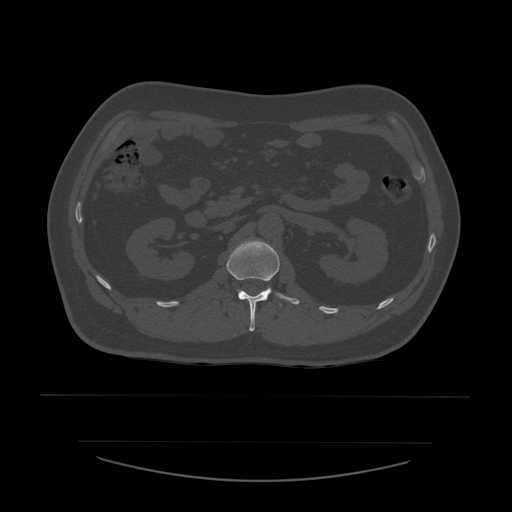
CT including the spine, one axial slice. Position 222 of 532 along the scan axis. Reconstruction kernel STANDARD. Bone window (W 1800 / L 400 HU). 1.25 mm slice thickness. 512 × 512 image matrix, field of view 441 × 441 mm. Patient age 44 years. From the clinical record (not read from this slice): primary cancer: soft tissue sarcoma.
Structures marked on this image (semi-automatically segmented with operator editing):
- L1 vertebra: bounding box [x1, y1, x2, y2] px = [227, 240, 300, 332]